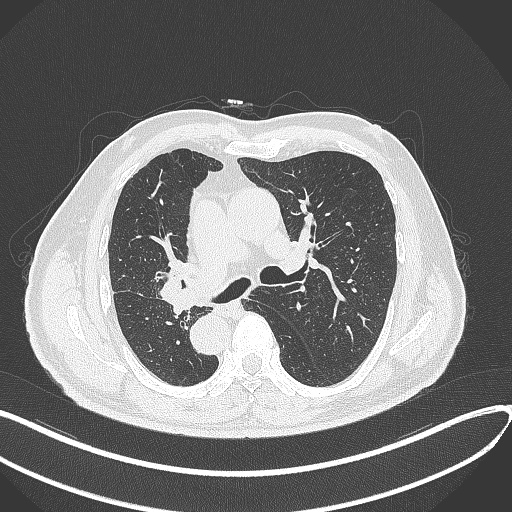
Chest CT, one axial slice. Slice 179 of 300 in the series (ordered by position). Reconstruction kernel B70f. Lung window (W 1500 / L -600 HU). 1 mm slice thickness. 512 × 512 image matrix. Male patient, age 67 years. From the clinical record (not read from this slice): clinical TNM (as recorded): T2a N0 M0.
Annotated regions visible in this slice (rectangle marked by the reading radiologist):
- lung tumour (recorded histology: squamous cell carcinoma): box from (x=151, y=256) to (x=206, y=313) px